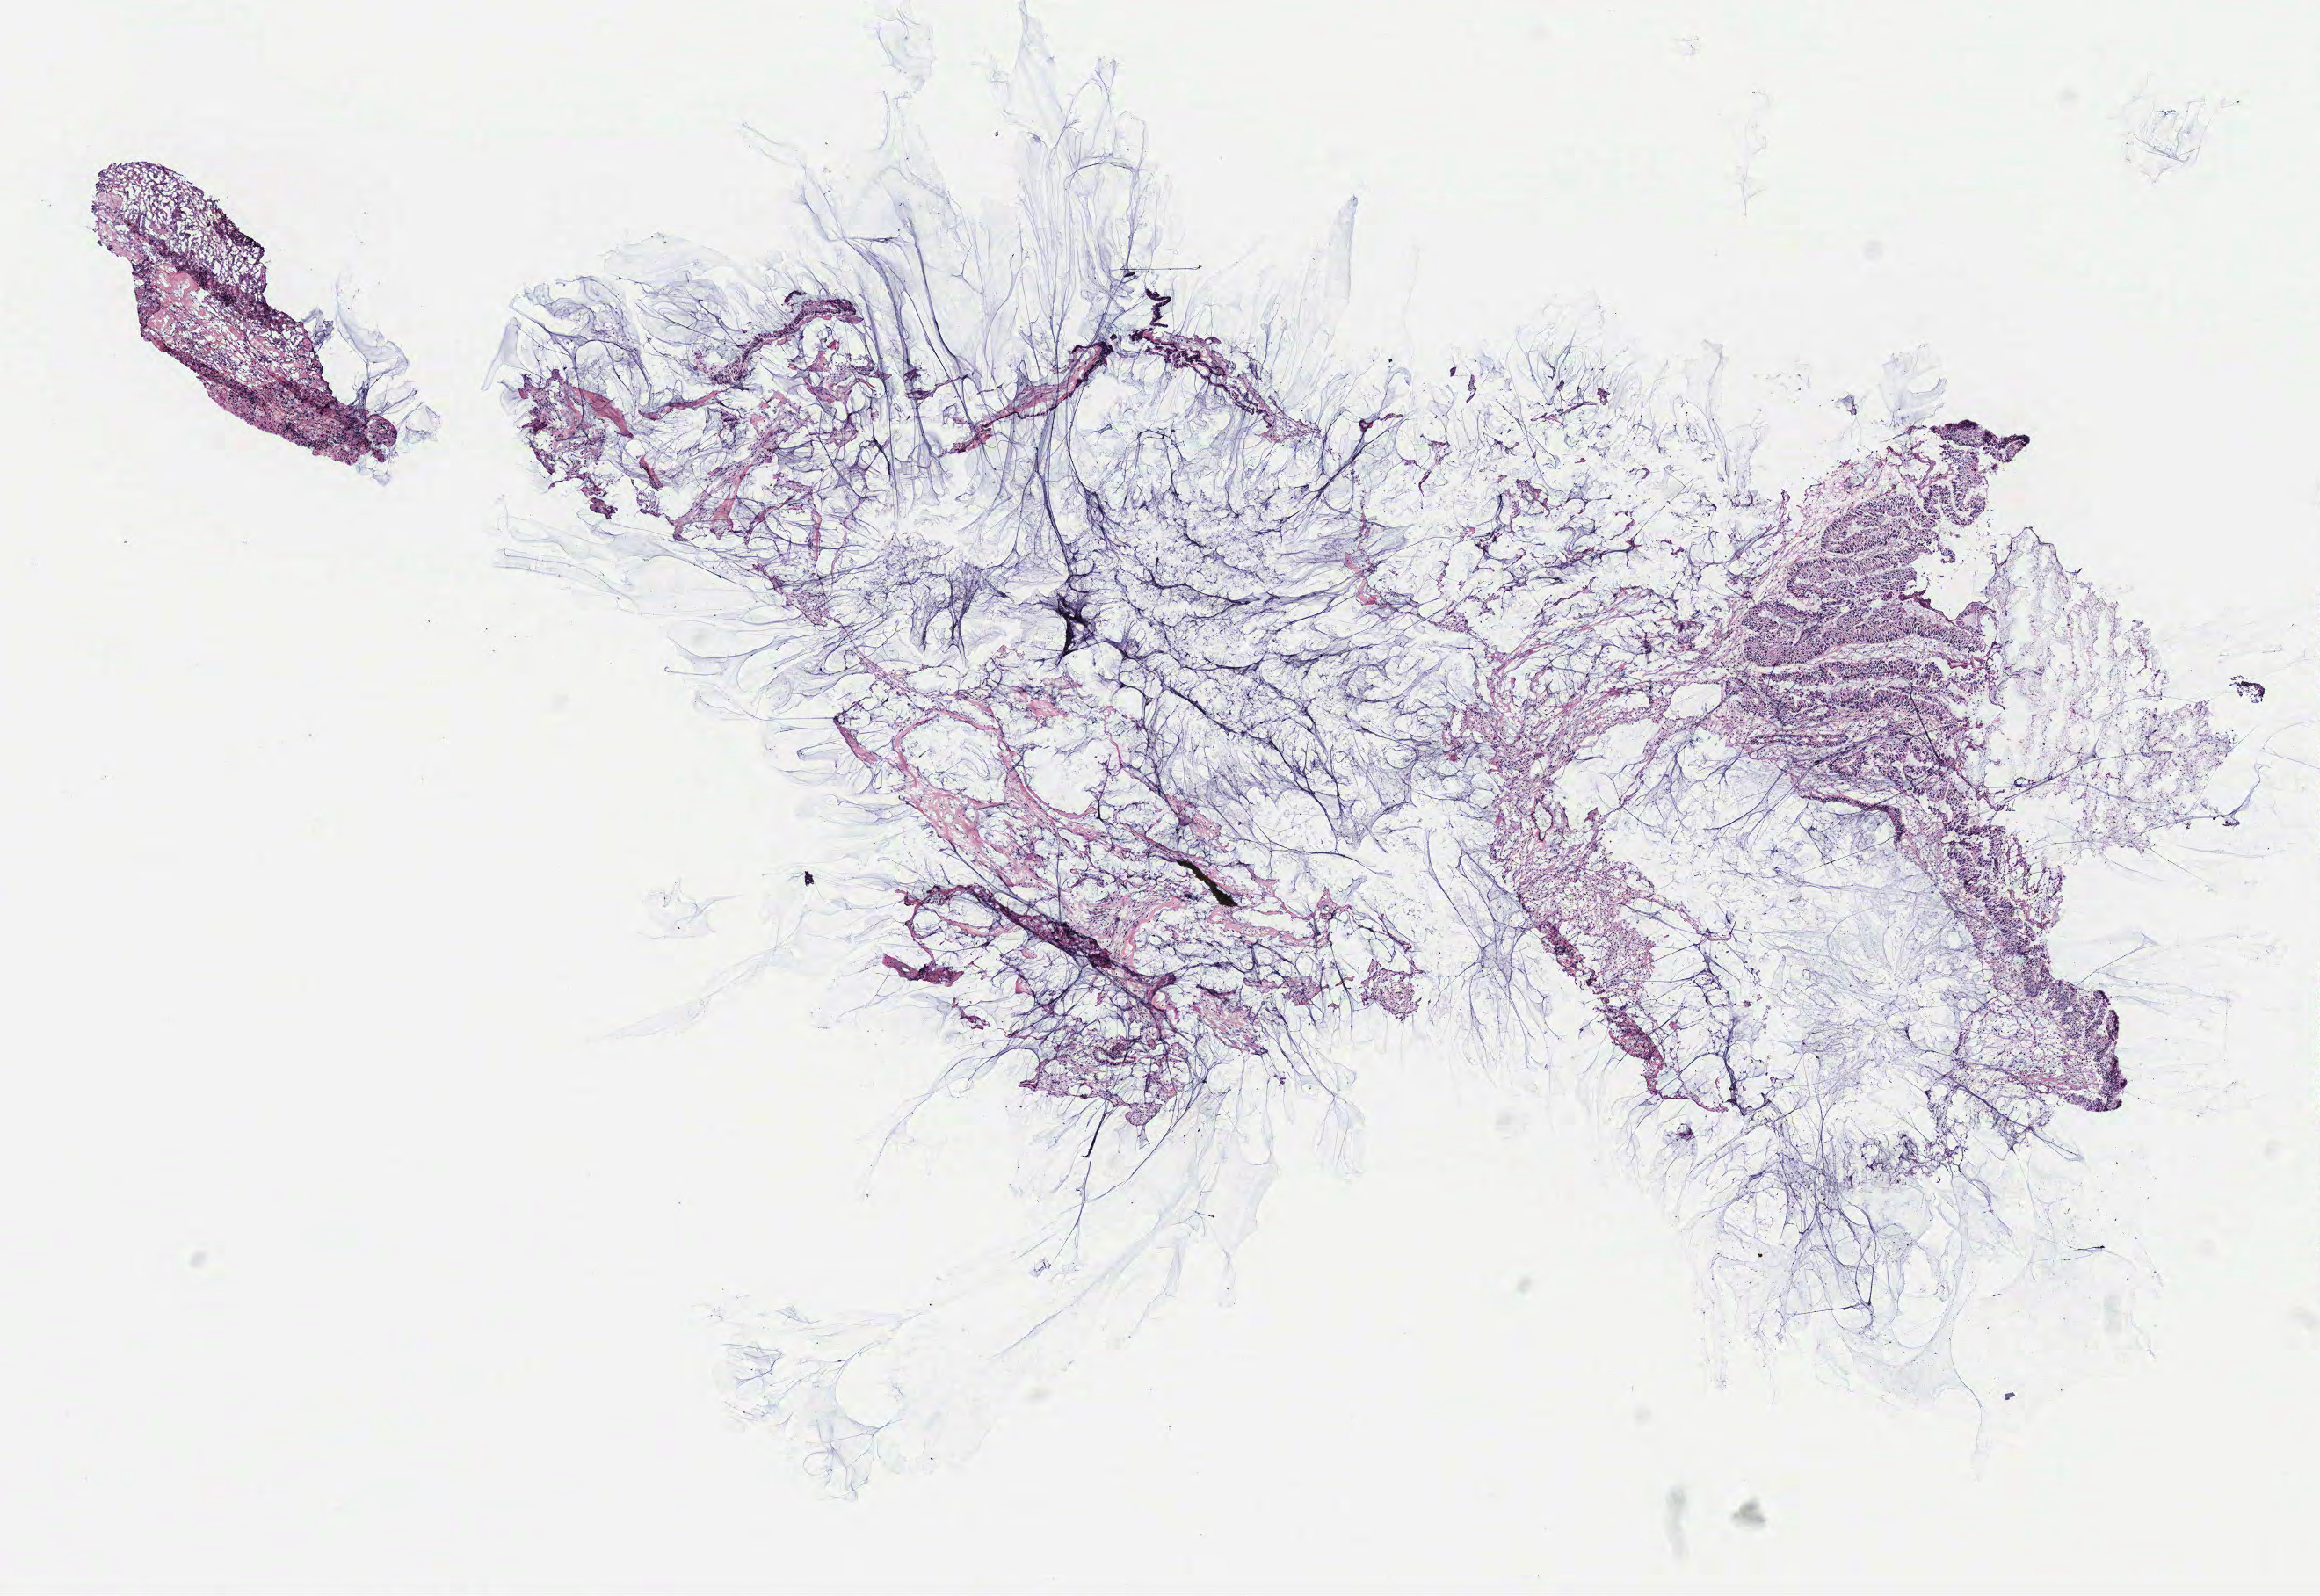
Whole-slide histology image, H&E-stained — a low-resolution overview of the entire scanned area, about 10.6 x 7.3 mm (from a 40x scan), colon, tissue type not recorded.
Patient diagnosis (cohort enrolment): colon cancer (colon).